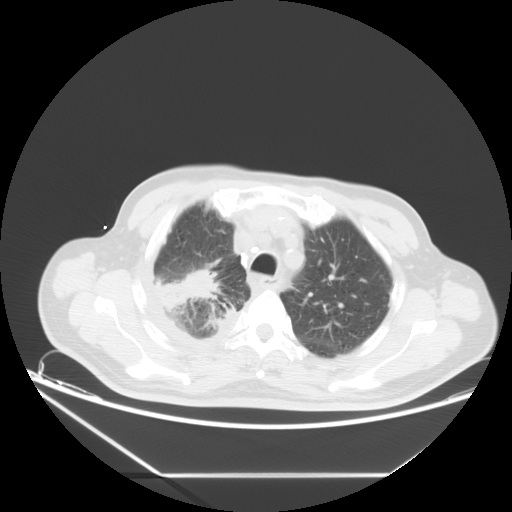
Chest CT, one axial slice; slice 13 of 20 in the series (ordered by position); reconstruction kernel STANDARD; lung window (W 1500 / L -600 HU); 5 mm slice thickness; 512 × 512 image matrix, field of view 418 × 418 mm. Patient: male, 75 years. From the clinical record (not read from this slice): clinical TNM (as recorded): T1c N1 M1.
Structures marked on this image (bounding box drawn by a radiologist):
- lung tumour (recorded histology: adenocarcinoma): bounding box [x1, y1, x2, y2] px = [148, 267, 223, 308]